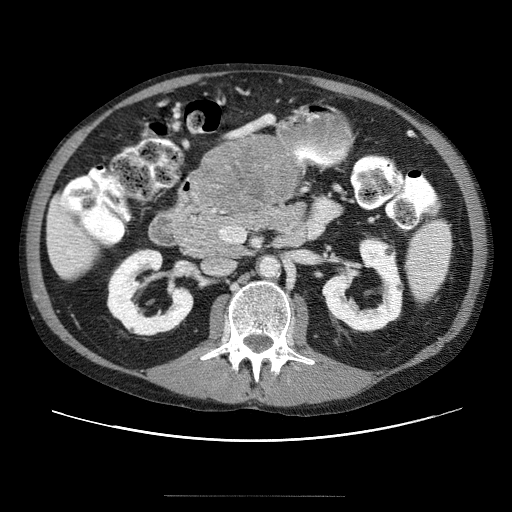
Contrast-enhanced abdominal CT (liver protocol), one axial slice. Reconstruction kernel STANDARD. 120 kVp. Soft-tissue window (W 400 / L 40 HU). 2.5 mm slice thickness. 512 × 512 image matrix, field of view 380 × 380 mm. Case-level facts recorded for this patient, not image findings: diagnosis: hepatocellular carcinoma (patient treated with transarterial chemoembolisation; whether this scan precedes or follows treatment is not stated here); TNM stage (as recorded): Stage-IVB; Child-Pugh class: B; tumour nodularity: multinodular.
Structures marked on this image (semi-automatic segmentation, software-assisted and operator-edited):
- liver parenchyma outside the tumour (the mass and vessels are separate outlines, so this box may not span the whole liver): box from (x=46, y=141) to (x=294, y=276) px
- mass: (x=191, y=140)–(x=297, y=217)
- liver vessels: (x=59, y=244)–(x=64, y=269)